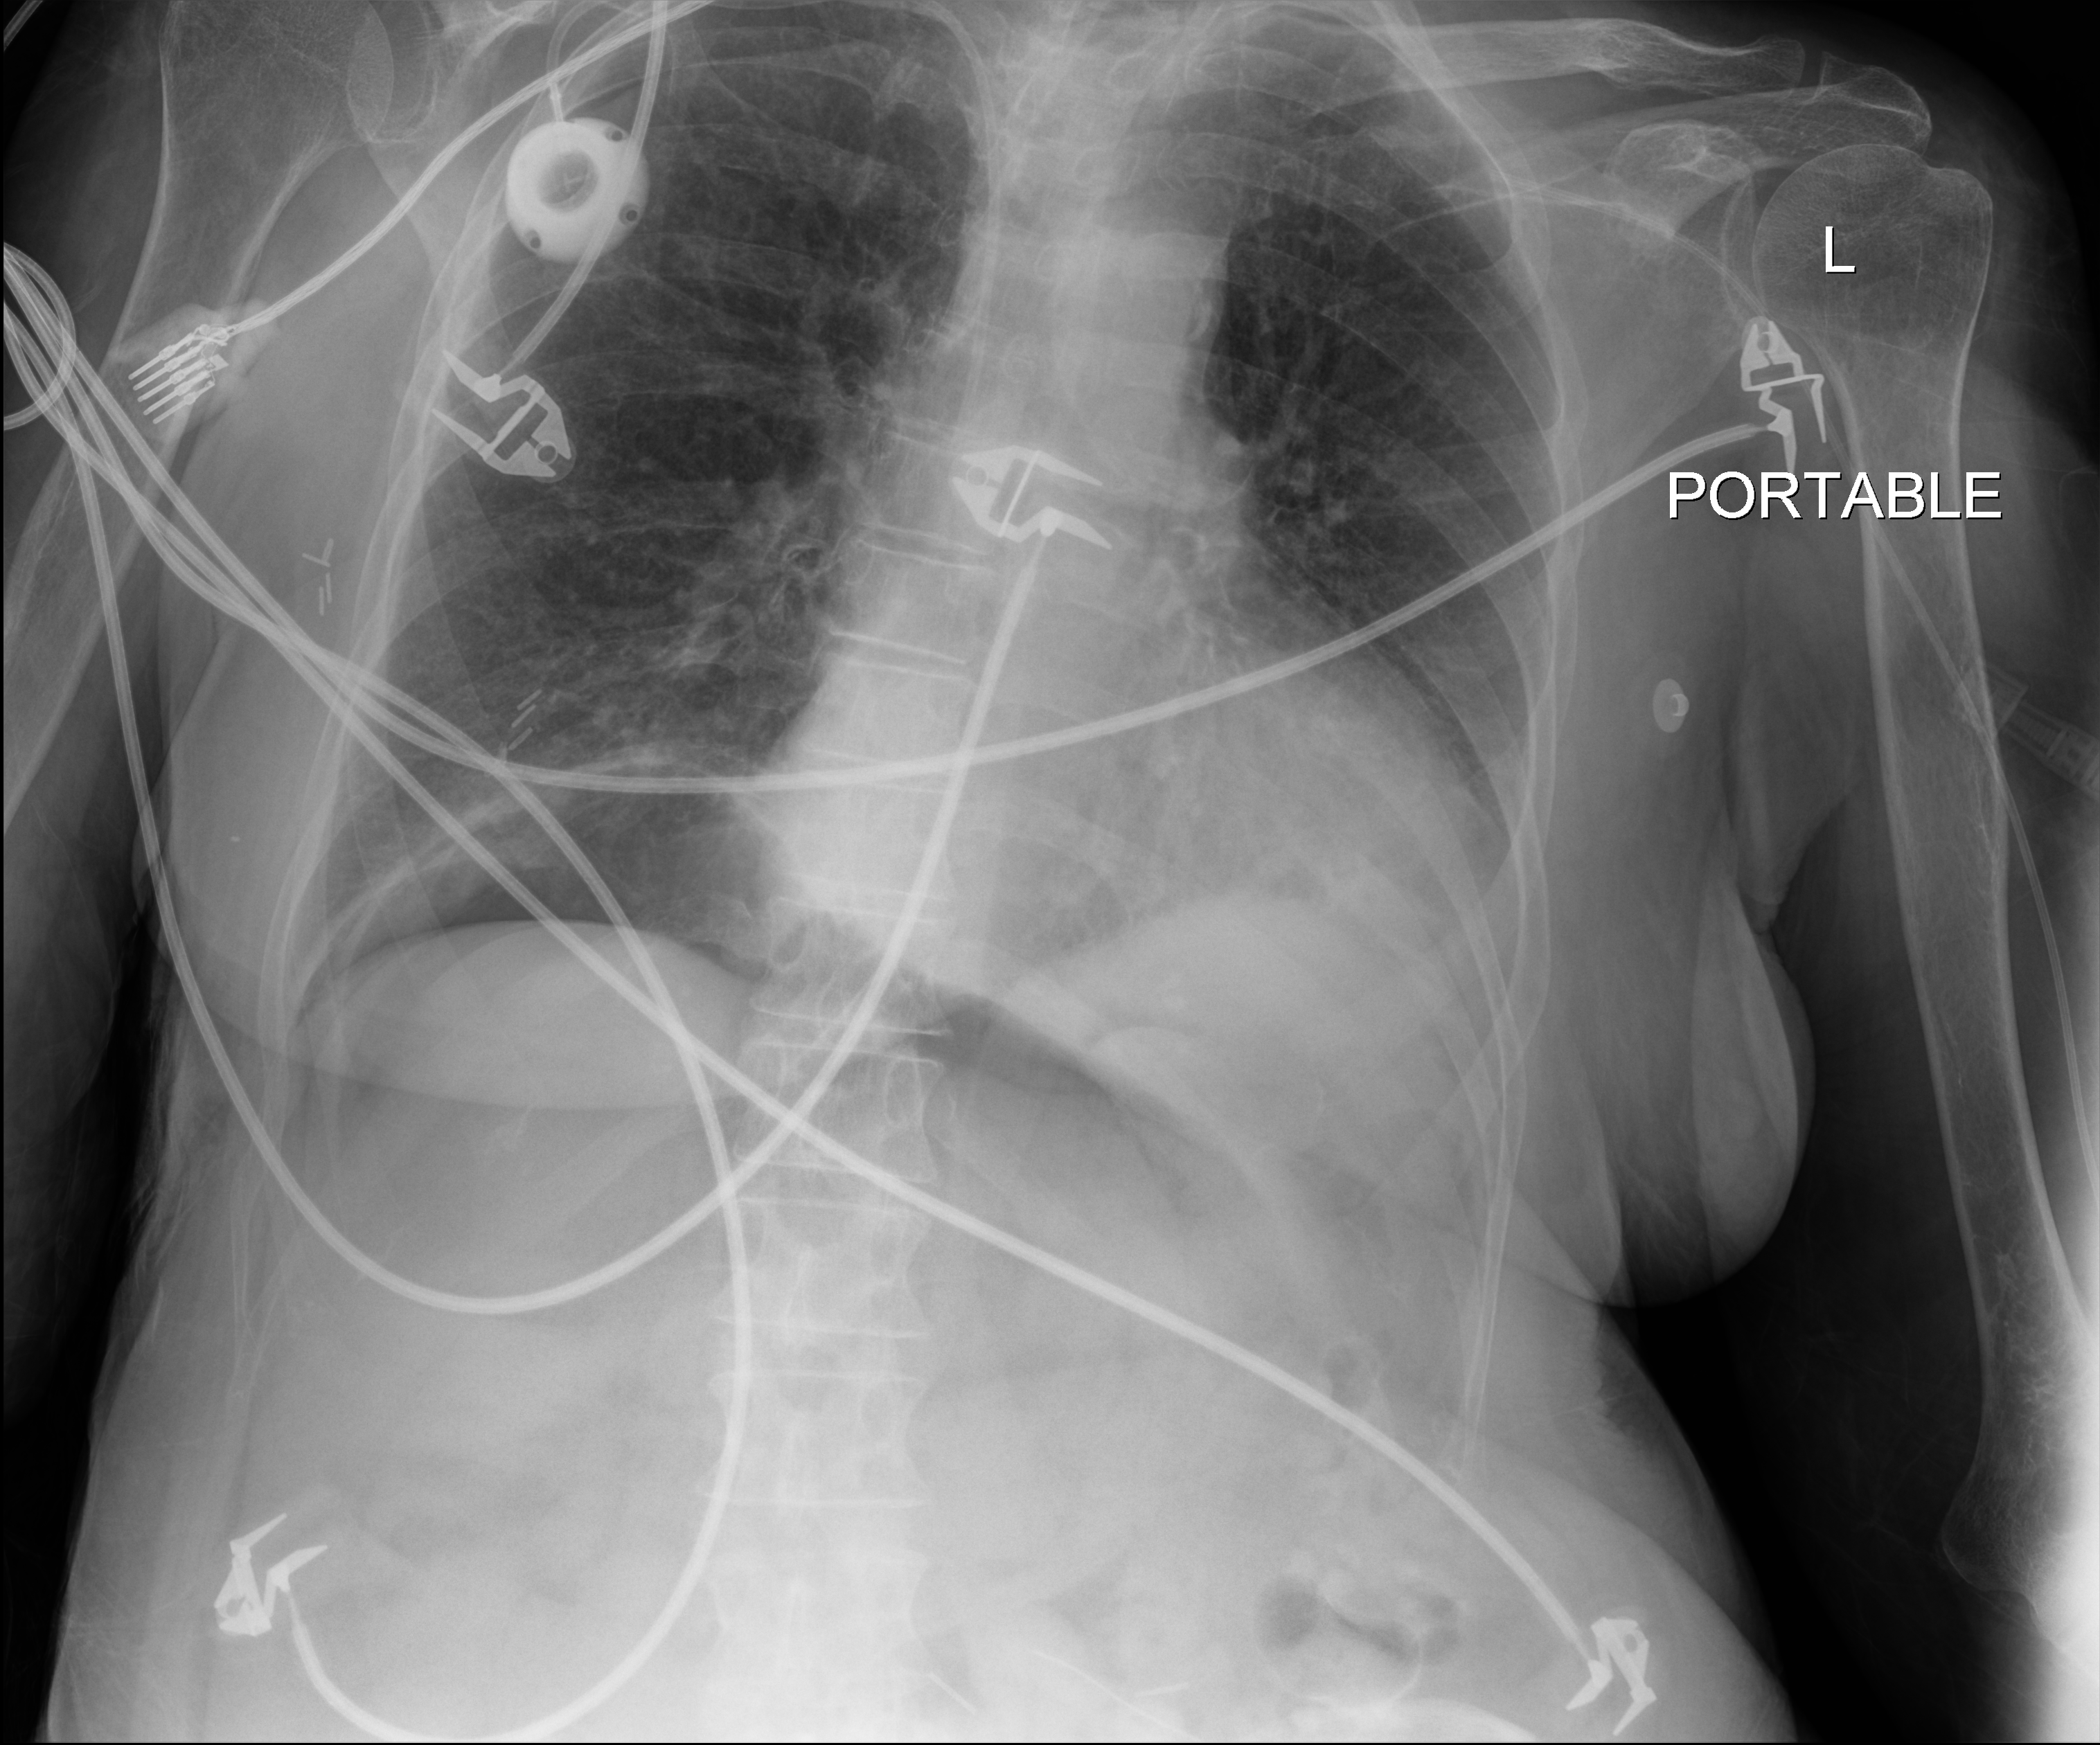
Bedside chest radiograph (digital radiography); anteroposterior (AP) projection. Patient hospitalised with COVID-19; female, aged 60–74 years.
From the hospital-stay record, not from the radiograph (when in the stay this image was taken is not recorded):
- hypertension (admission record): yes